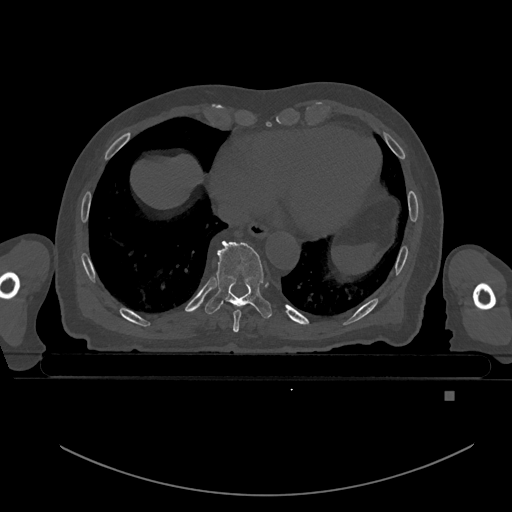
CT including the spine, one axial slice; position 158 of 969 along the scan axis; bone window (W 1800 / L 400 HU); 0.5 mm slice thickness; 512 × 512 image matrix. Patient: male, 82 years. Case-level facts recorded for this patient, not image findings: primary cancer: prostate; vertebrae with lytic lesions (as recorded): T11, T9, T8, T2.
Outlined on this slice (semi-automatic segmentation, software-assisted and operator-edited):
- T8 vertebra: box from (x=233, y=306) to (x=242, y=333) px
- T9 vertebra: (x=205, y=240)–(x=272, y=319)